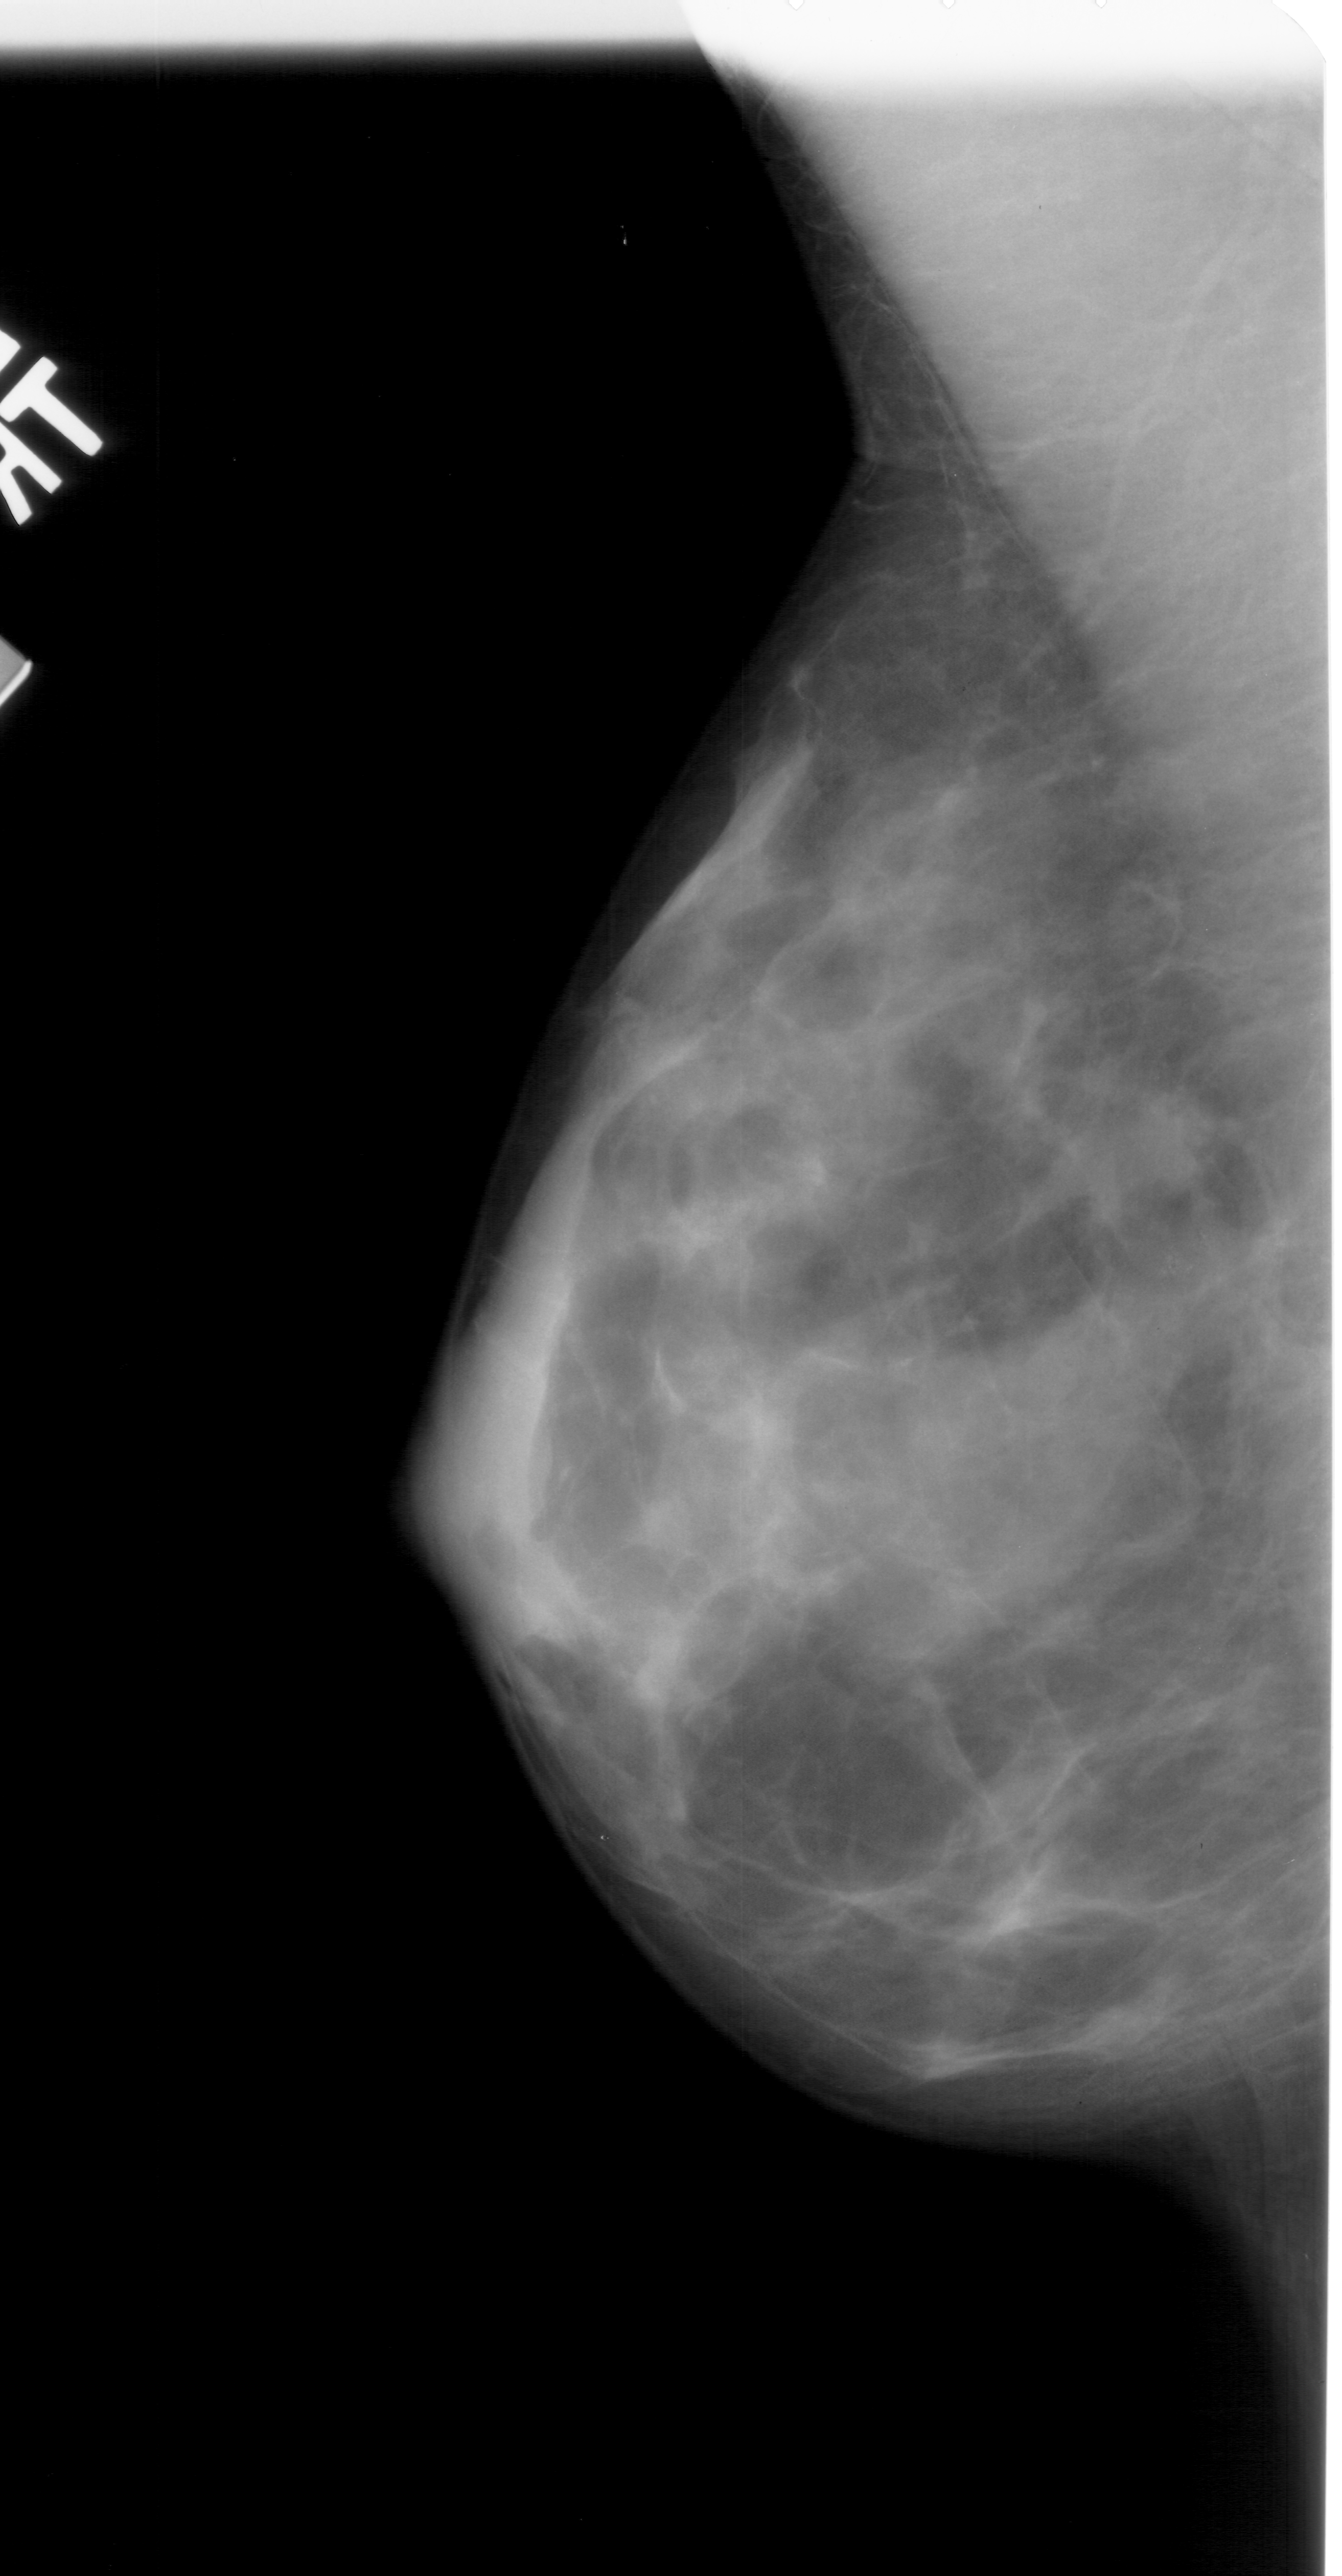
Mammogram (digitized film); left breast; MLO view; BI-RADS breast density category 4 (scale 1–4).
Finding: calcifications, morphology pleomorphic, distribution clustered; BI-RADS assessment category 4; pathology result (as recorded, not read from the image): benign.